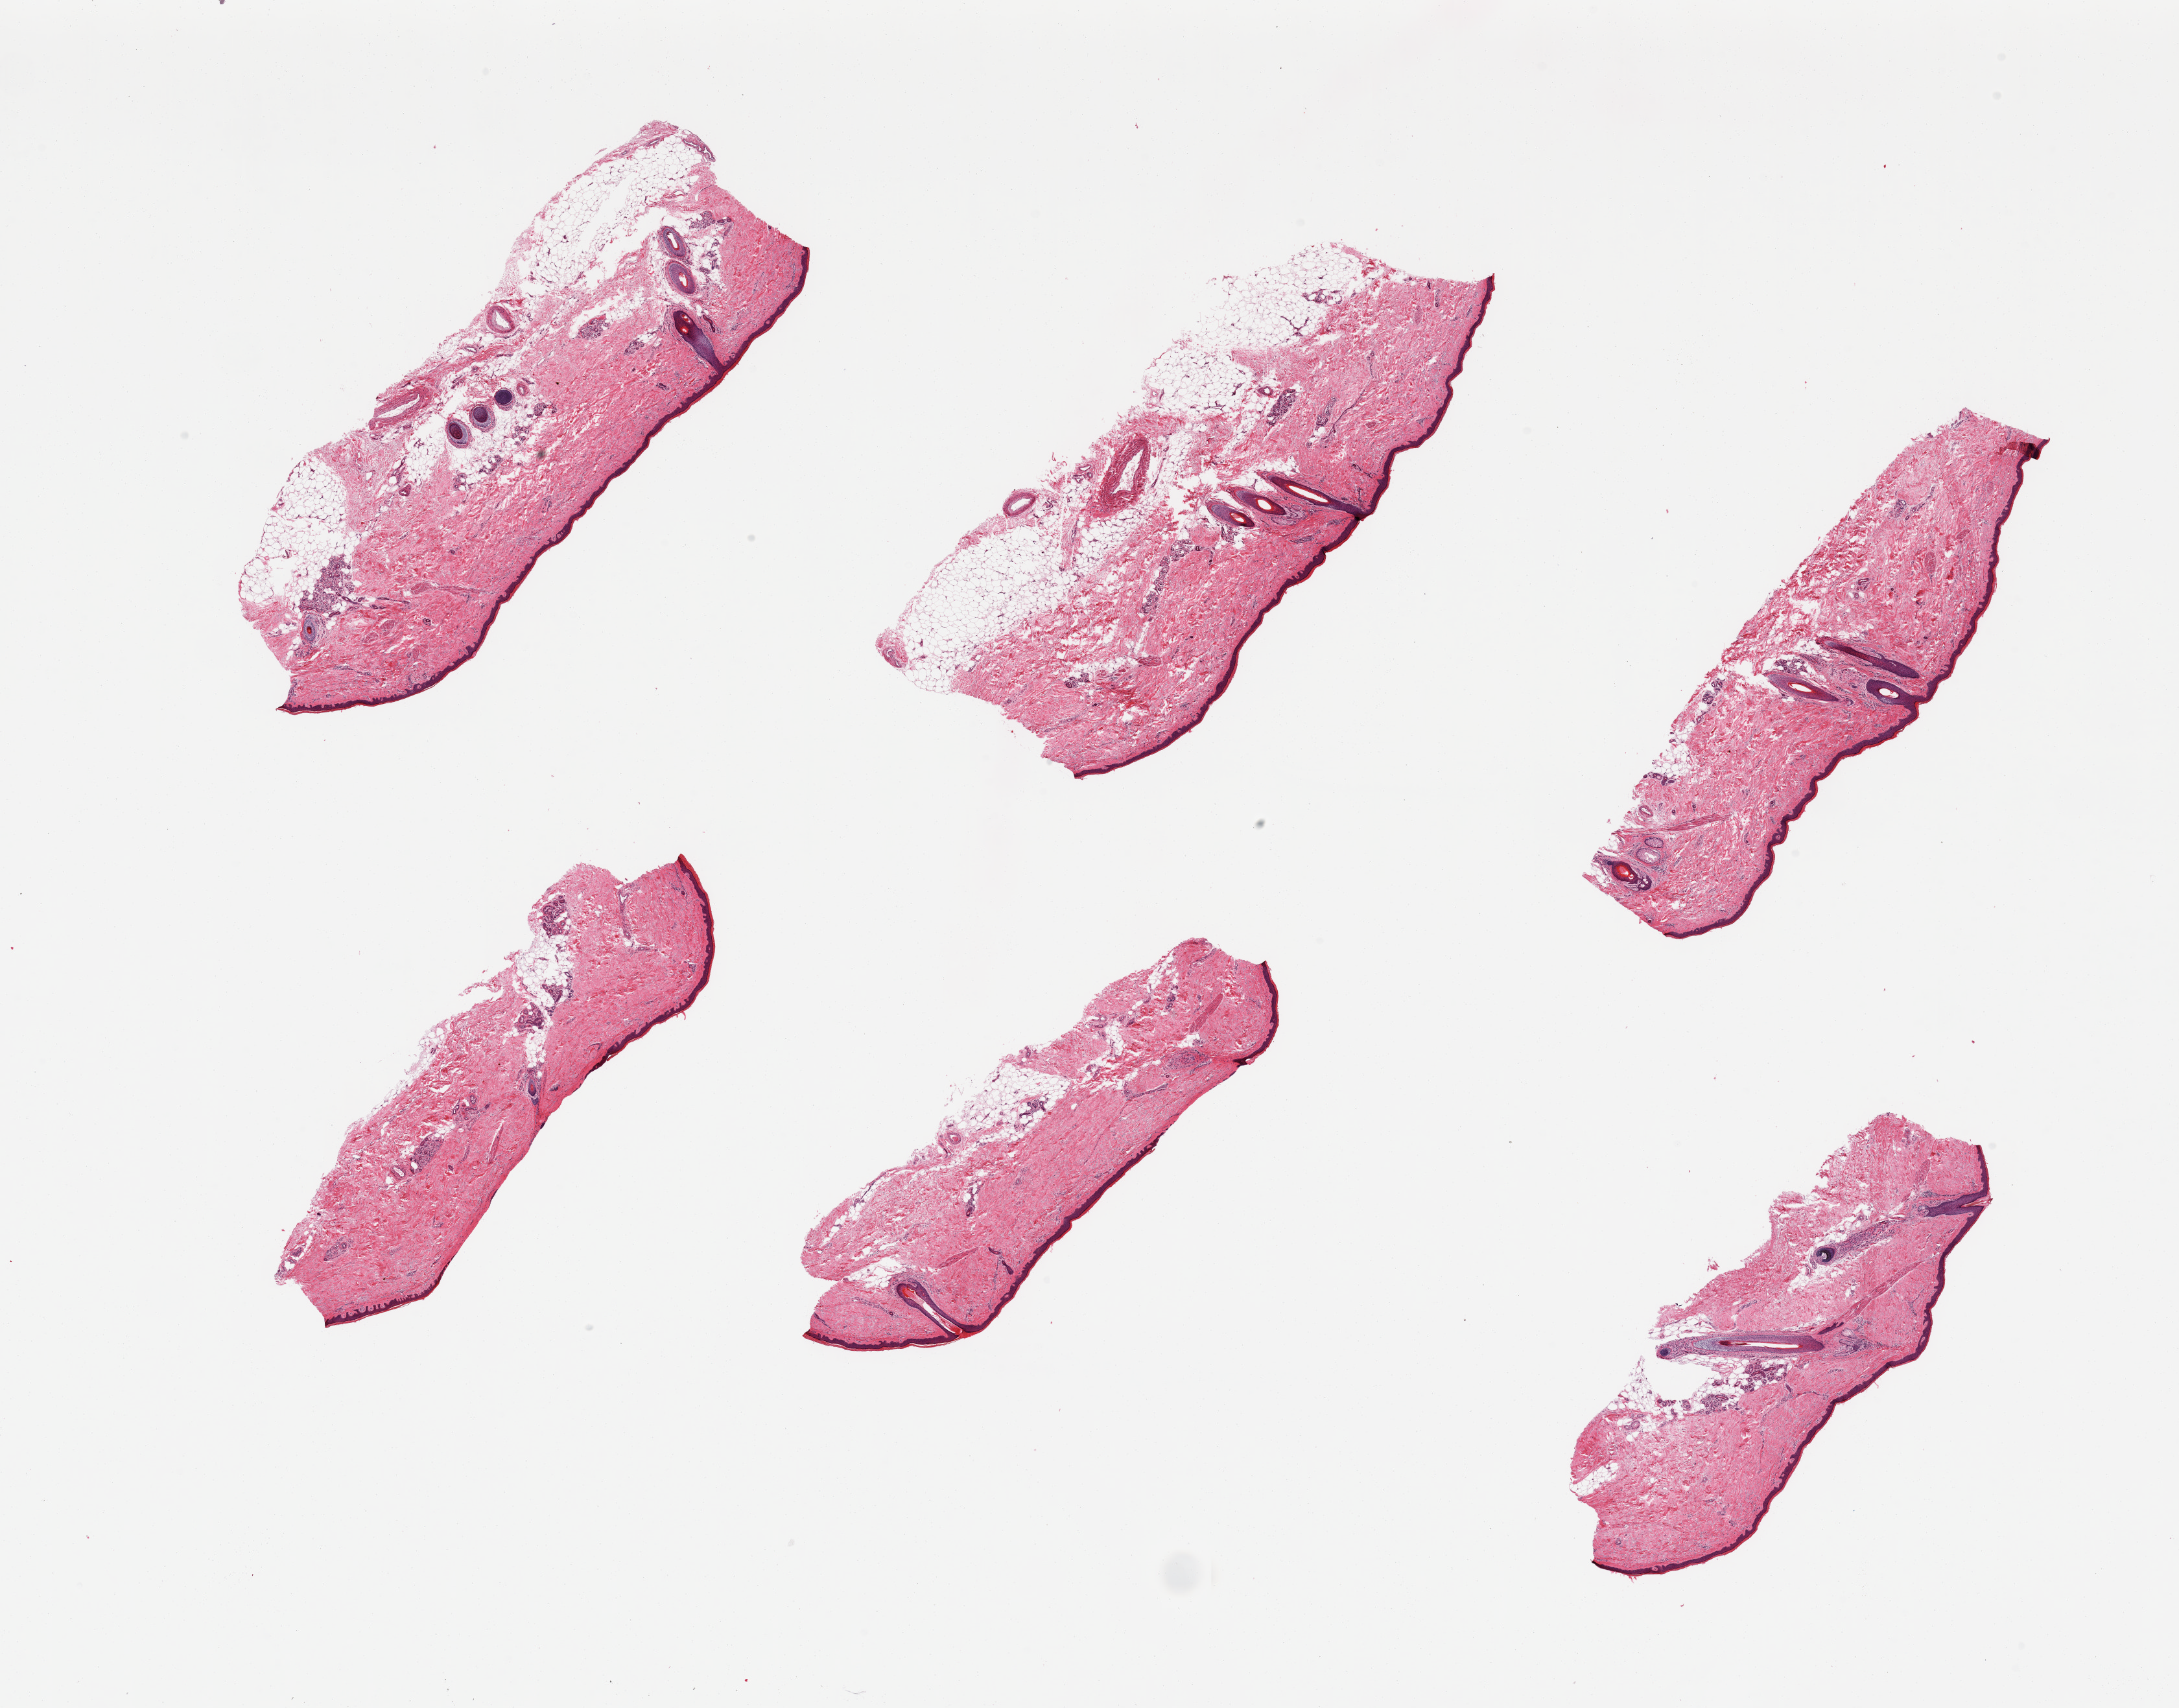
Digitized hematoxylin and eosin (H&E)-stained section, a low-resolution overview of the entire scanned area, about 26.6 x 20.8 mm; PAXgene-fixed paraffin-embedded (PFPE) section; target tissue: skin of lower leg; tissue donor sample. Male donor.
• pathologist's review note for this sample: 6 pieces; up to 4 hair follicles per piece; 10 to 40% dermal fat